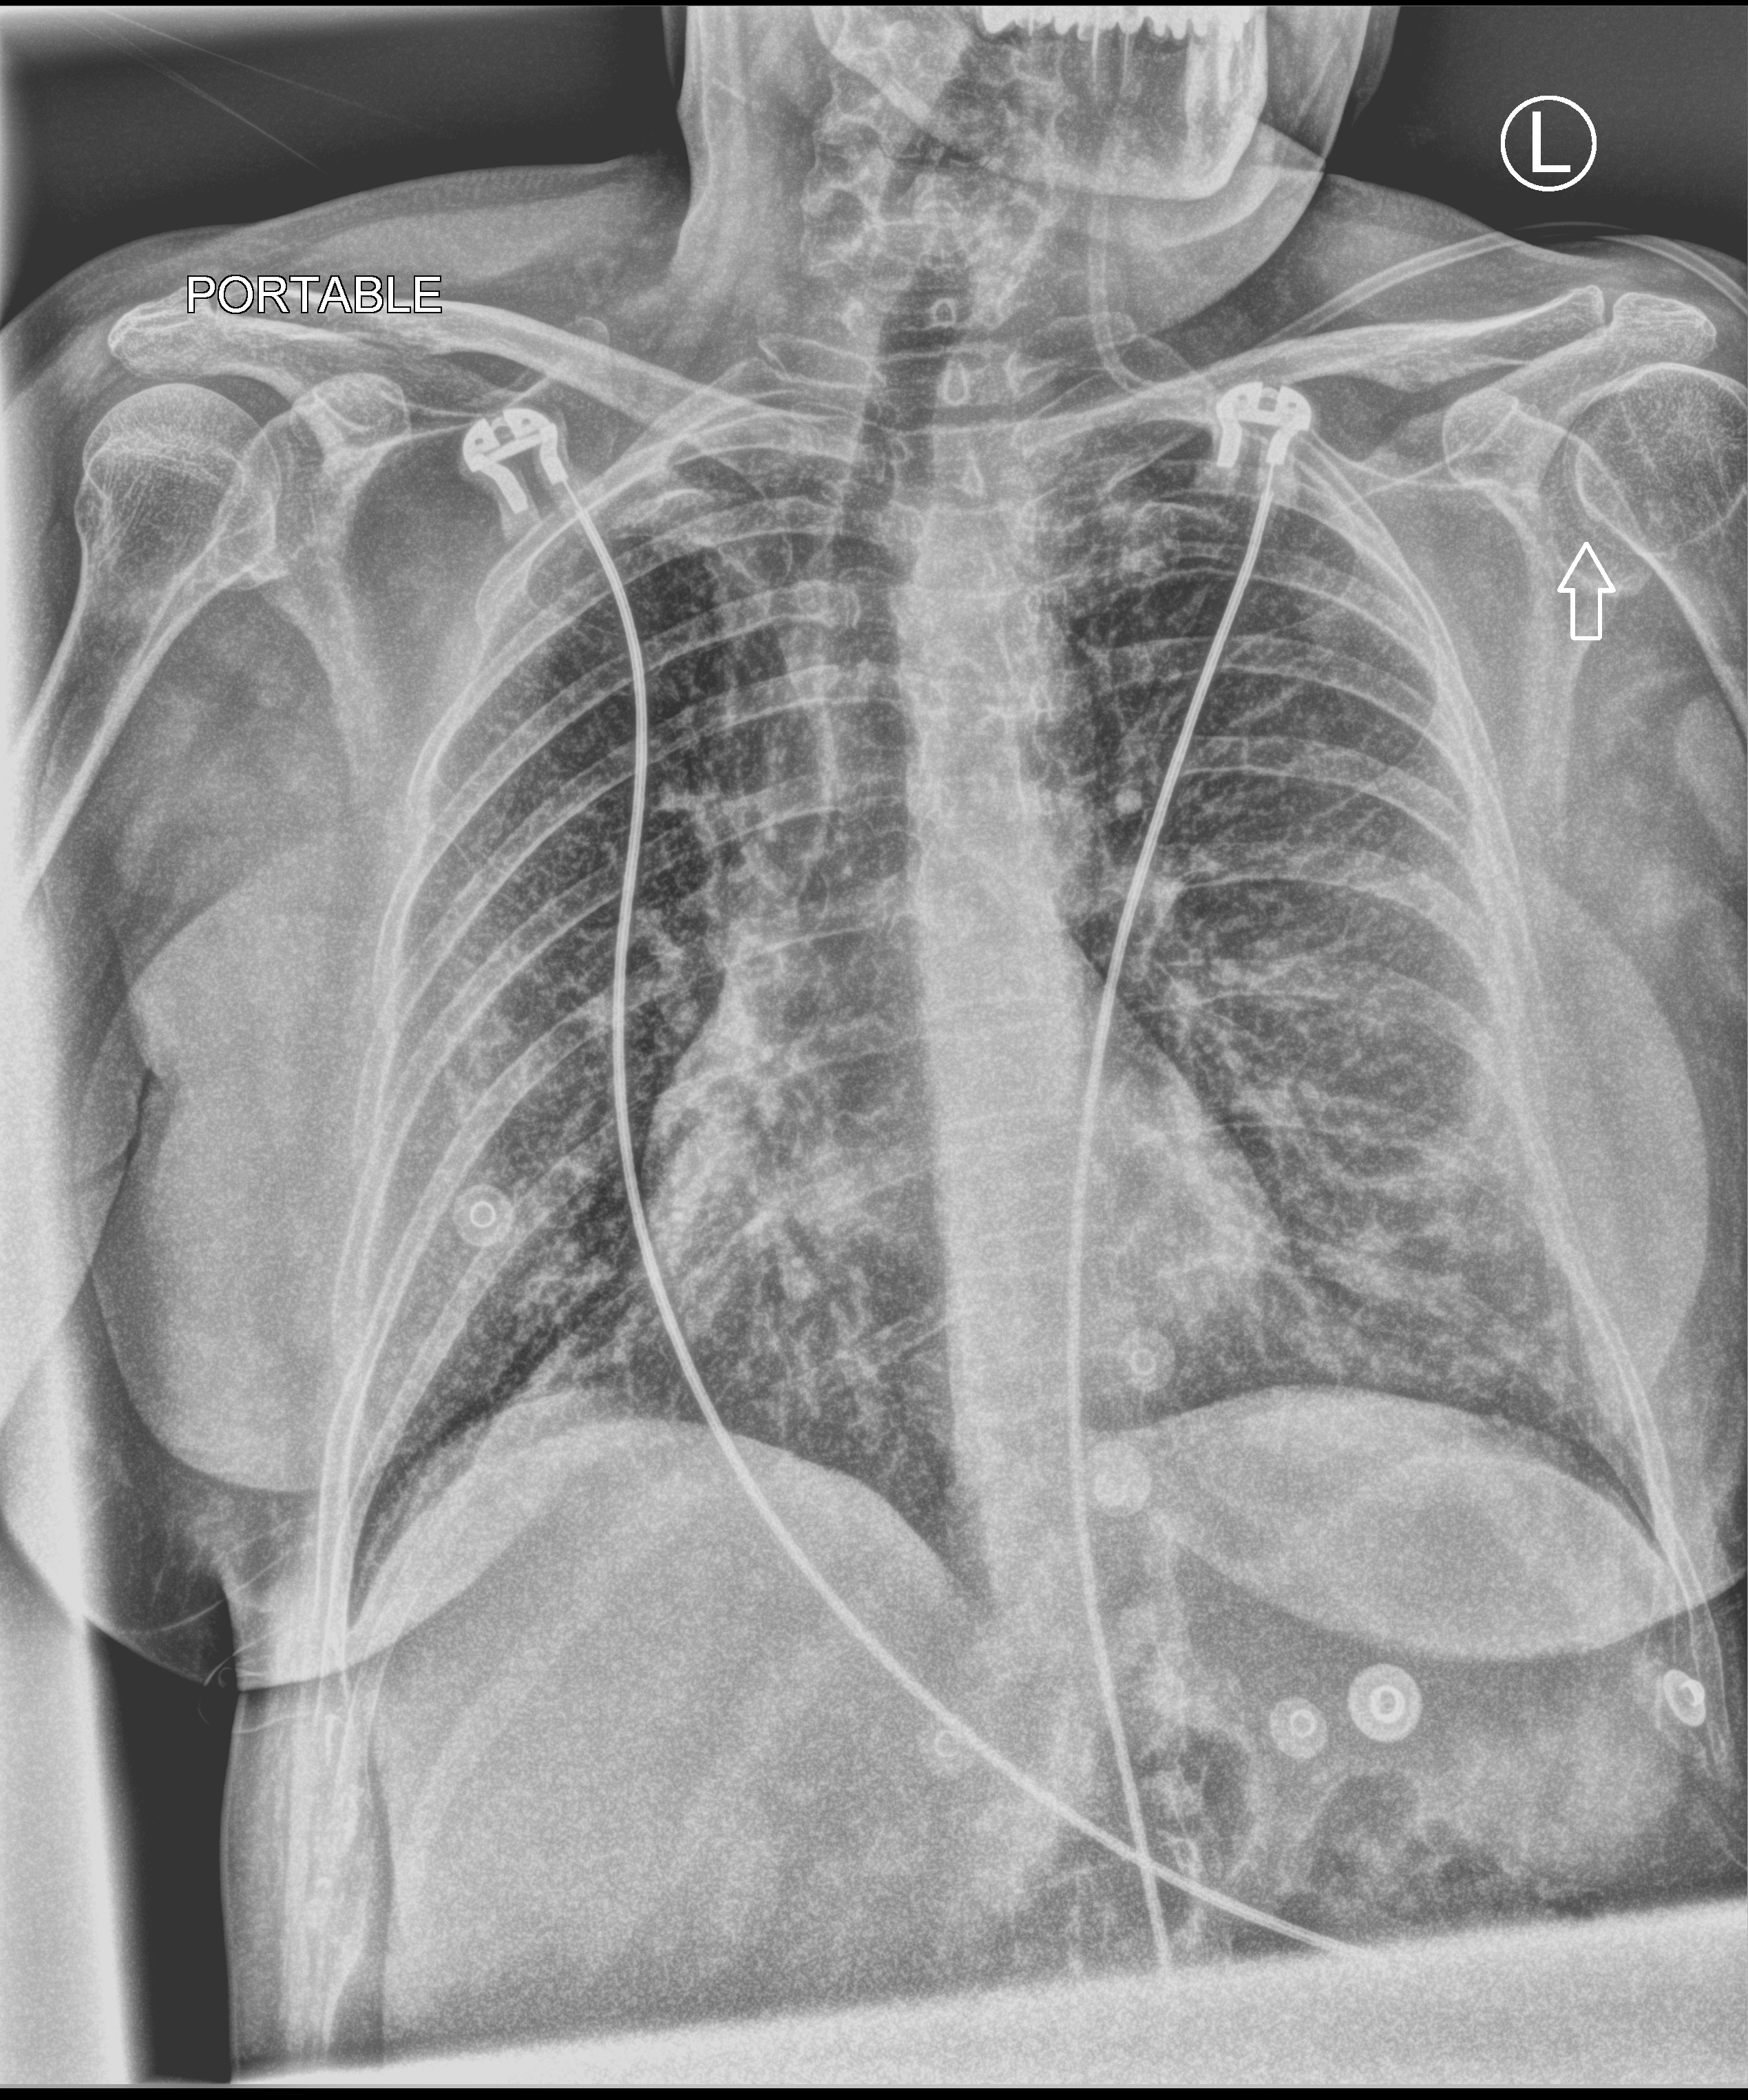
Portable chest radiograph, anteroposterior (AP) projection. Patient hospitalised with COVID-19; female, aged 60–74 years.
From the hospital-stay record, not from the radiograph (when in the stay this image was taken is not recorded): other chronic lung disease (admission record): no; hypertension (admission record): no; mechanically ventilated during this hospital stay: no.